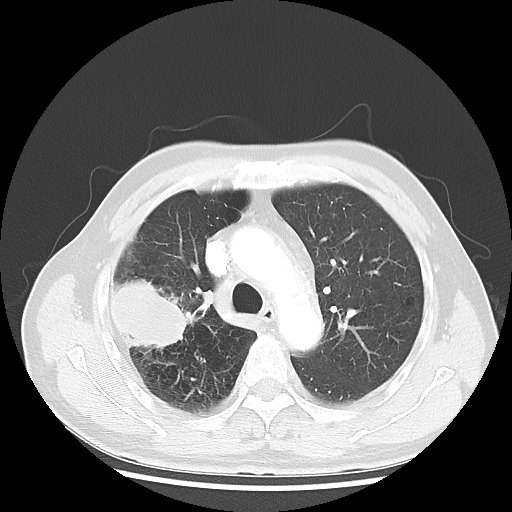
Chest CT, one axial slice; slice 35 of 50 in the series (ordered by position); lung window (W 1500 / L -600 HU); 5 mm slice thickness; 512 × 512 image matrix, field of view 360 × 360 mm. Patient: male, 69 years. From the clinical record (not read from this slice): clinical TNM (as recorded): T3 N0 M0; histopathological grade: G3.
Outlined on this slice (rectangle marked by the reading radiologist):
- lung tumour (recorded histology: adenocarcinoma): bounding box [x1, y1, x2, y2] px = [112, 274, 190, 350]